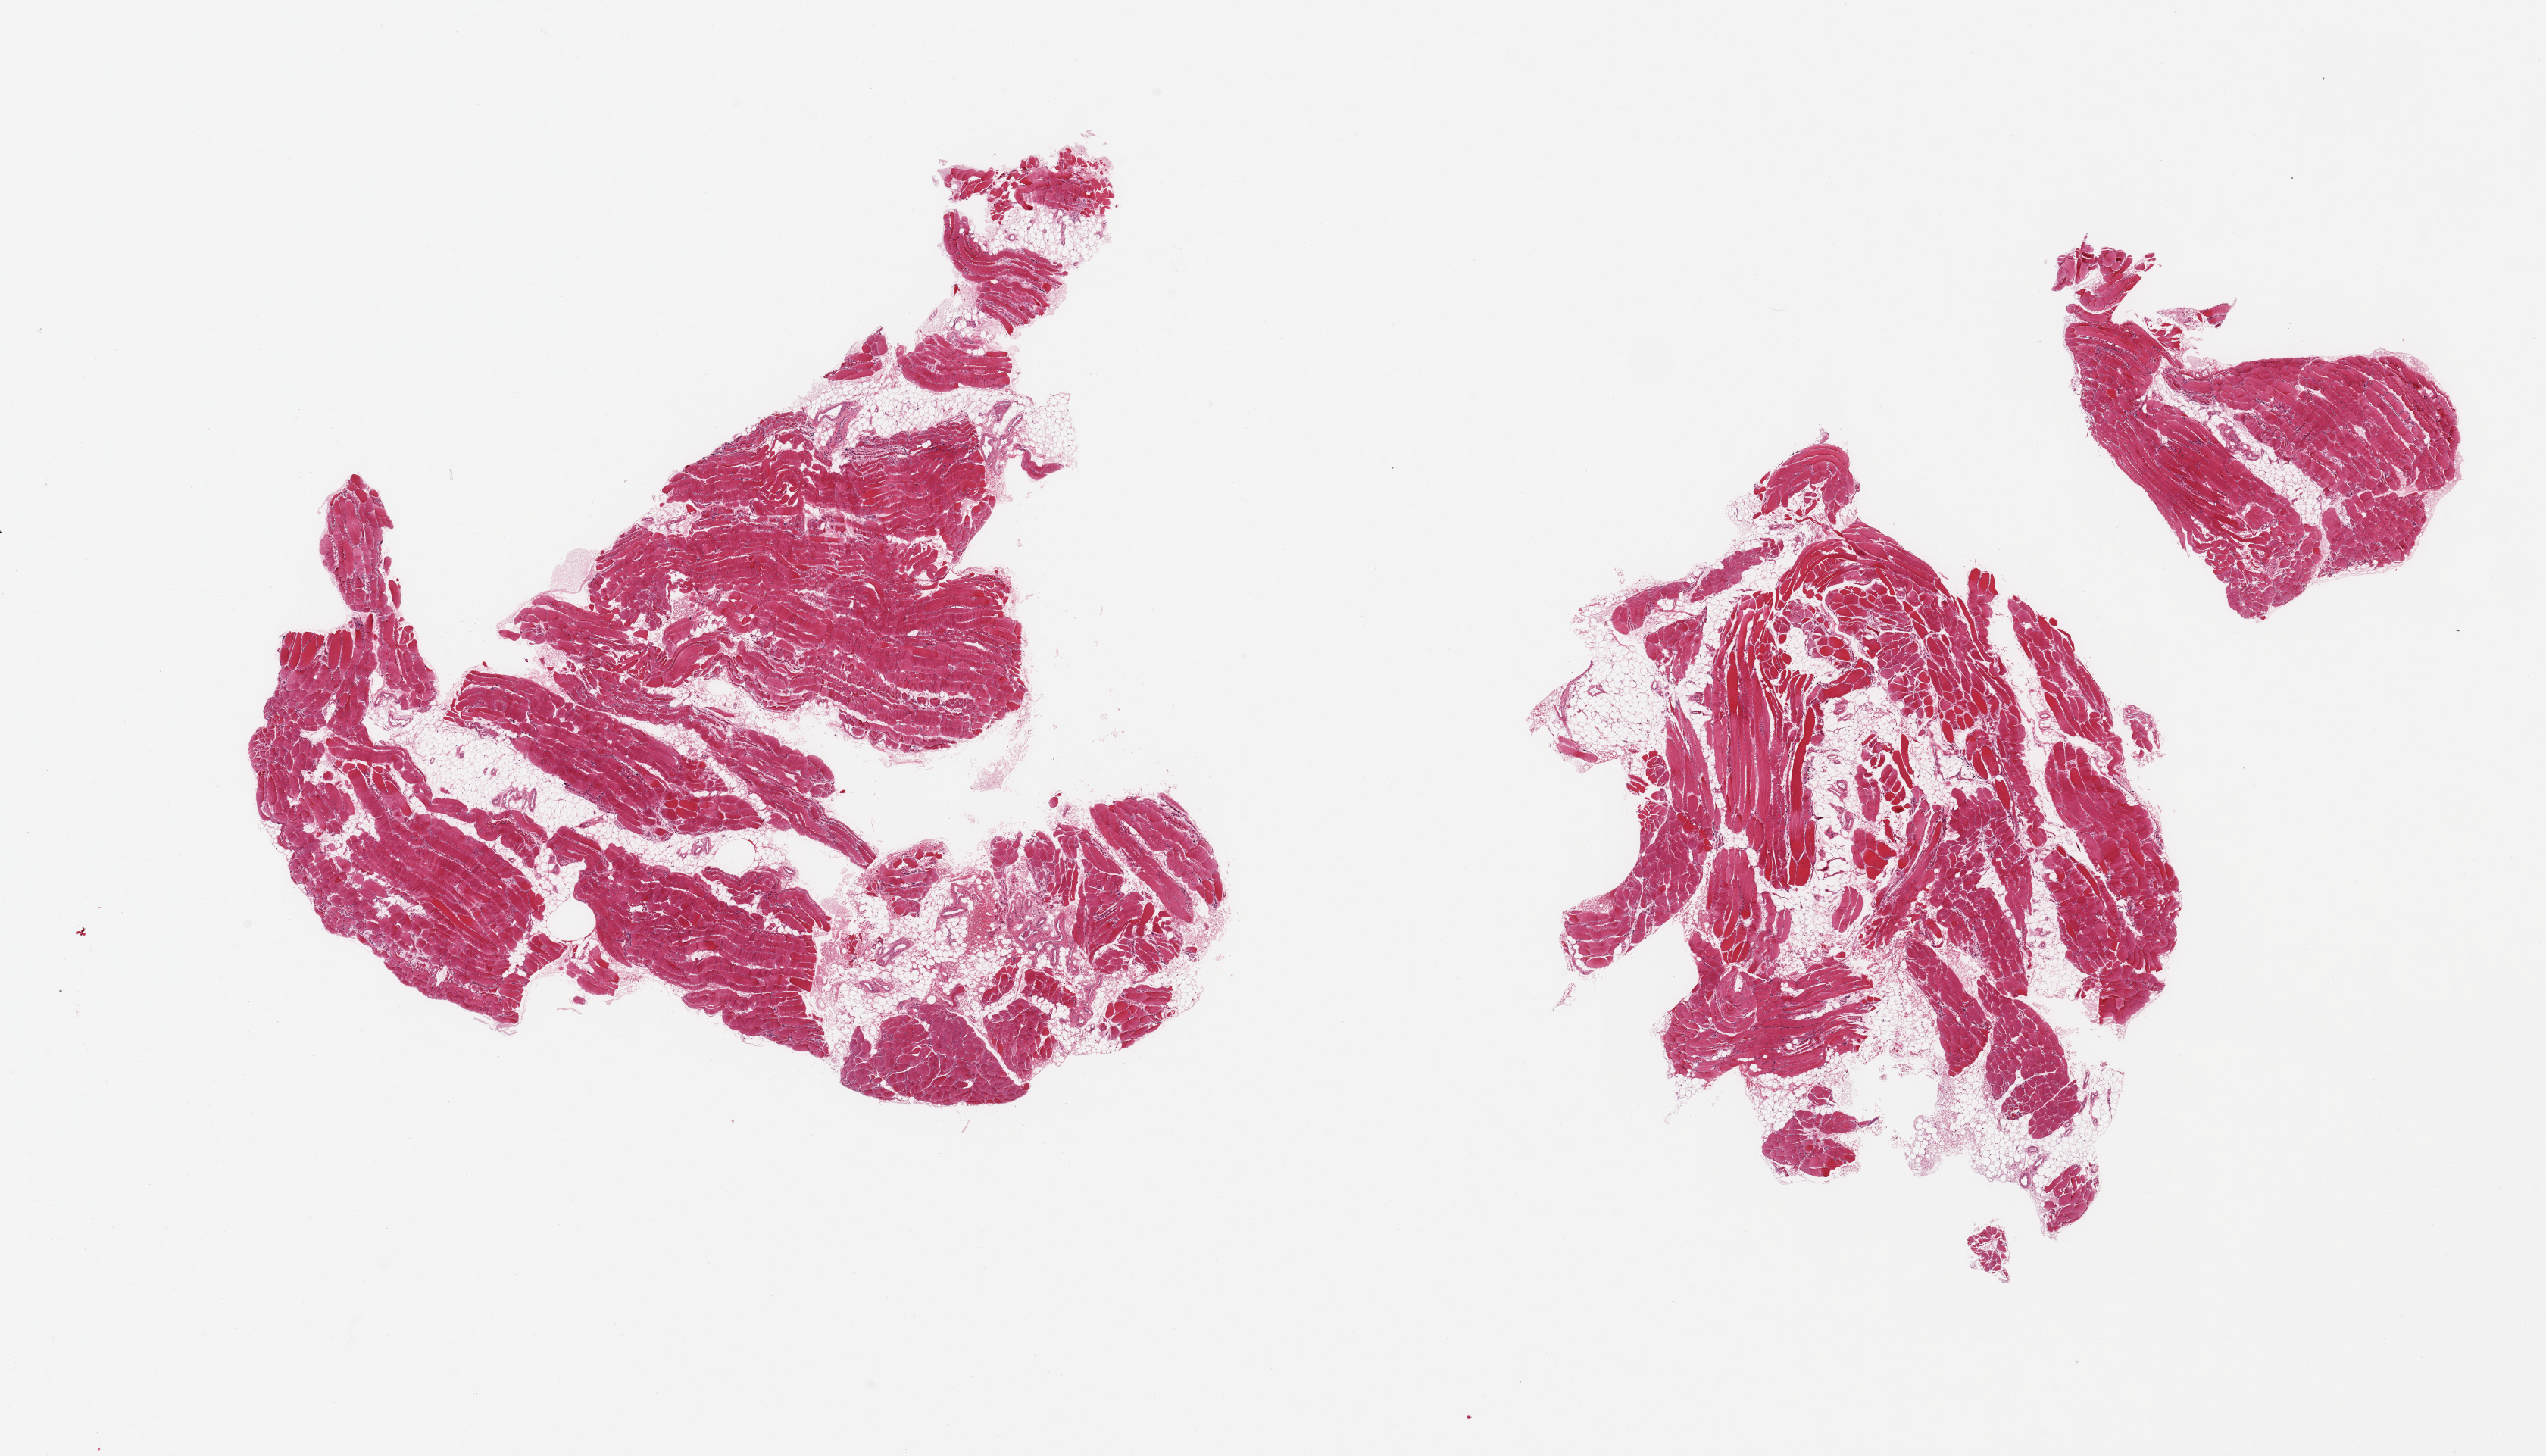
Whole-slide image, haematoxylin and eosin stain — shown as a low-resolution overview of the whole scanned area (about 26.6 x 15.2 mm, acquisition: 20x scan). PAXgene-fixed paraffin-embedded (PFPE) section. Target tissue: skeletal muscle. Donor tissue sample. Donor: male.
• reviewer comment on this tissue sample: 2 pieces, interstitial fat/vascular elements are ~35% of tissue